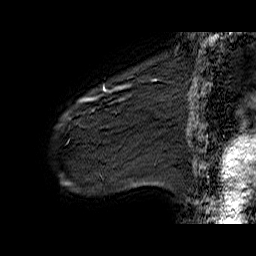
Breast MRI (dynamic contrast-enhanced), one sagittal slice. Dynamic contrast-enhanced series, time point 2 of 6 at this slice position (early post-contrast). 1.5 T. TE 6.4 ms, TR 32.9 ms. 4 mm slice thickness. 256 × 256 image matrix. Female patient. From the clinical record (not read from this slice): setting: breast cancer imaged before/during neoadjuvant chemotherapy; receptor status: HER2-positive.
Annotated regions visible in this slice (semi-automatic segmentation, software-assisted and operator-edited):
- analysis volume of interest (the breast-tissue region the enhancement analysis was run in; not a lesion): bounding box <61,77,141,142> (left, top, right, bottom; pixels)
- tumour enhancement mask (voxels above the 100 % enhancement threshold inside the analysis volume of interest): <80,85,130,102>